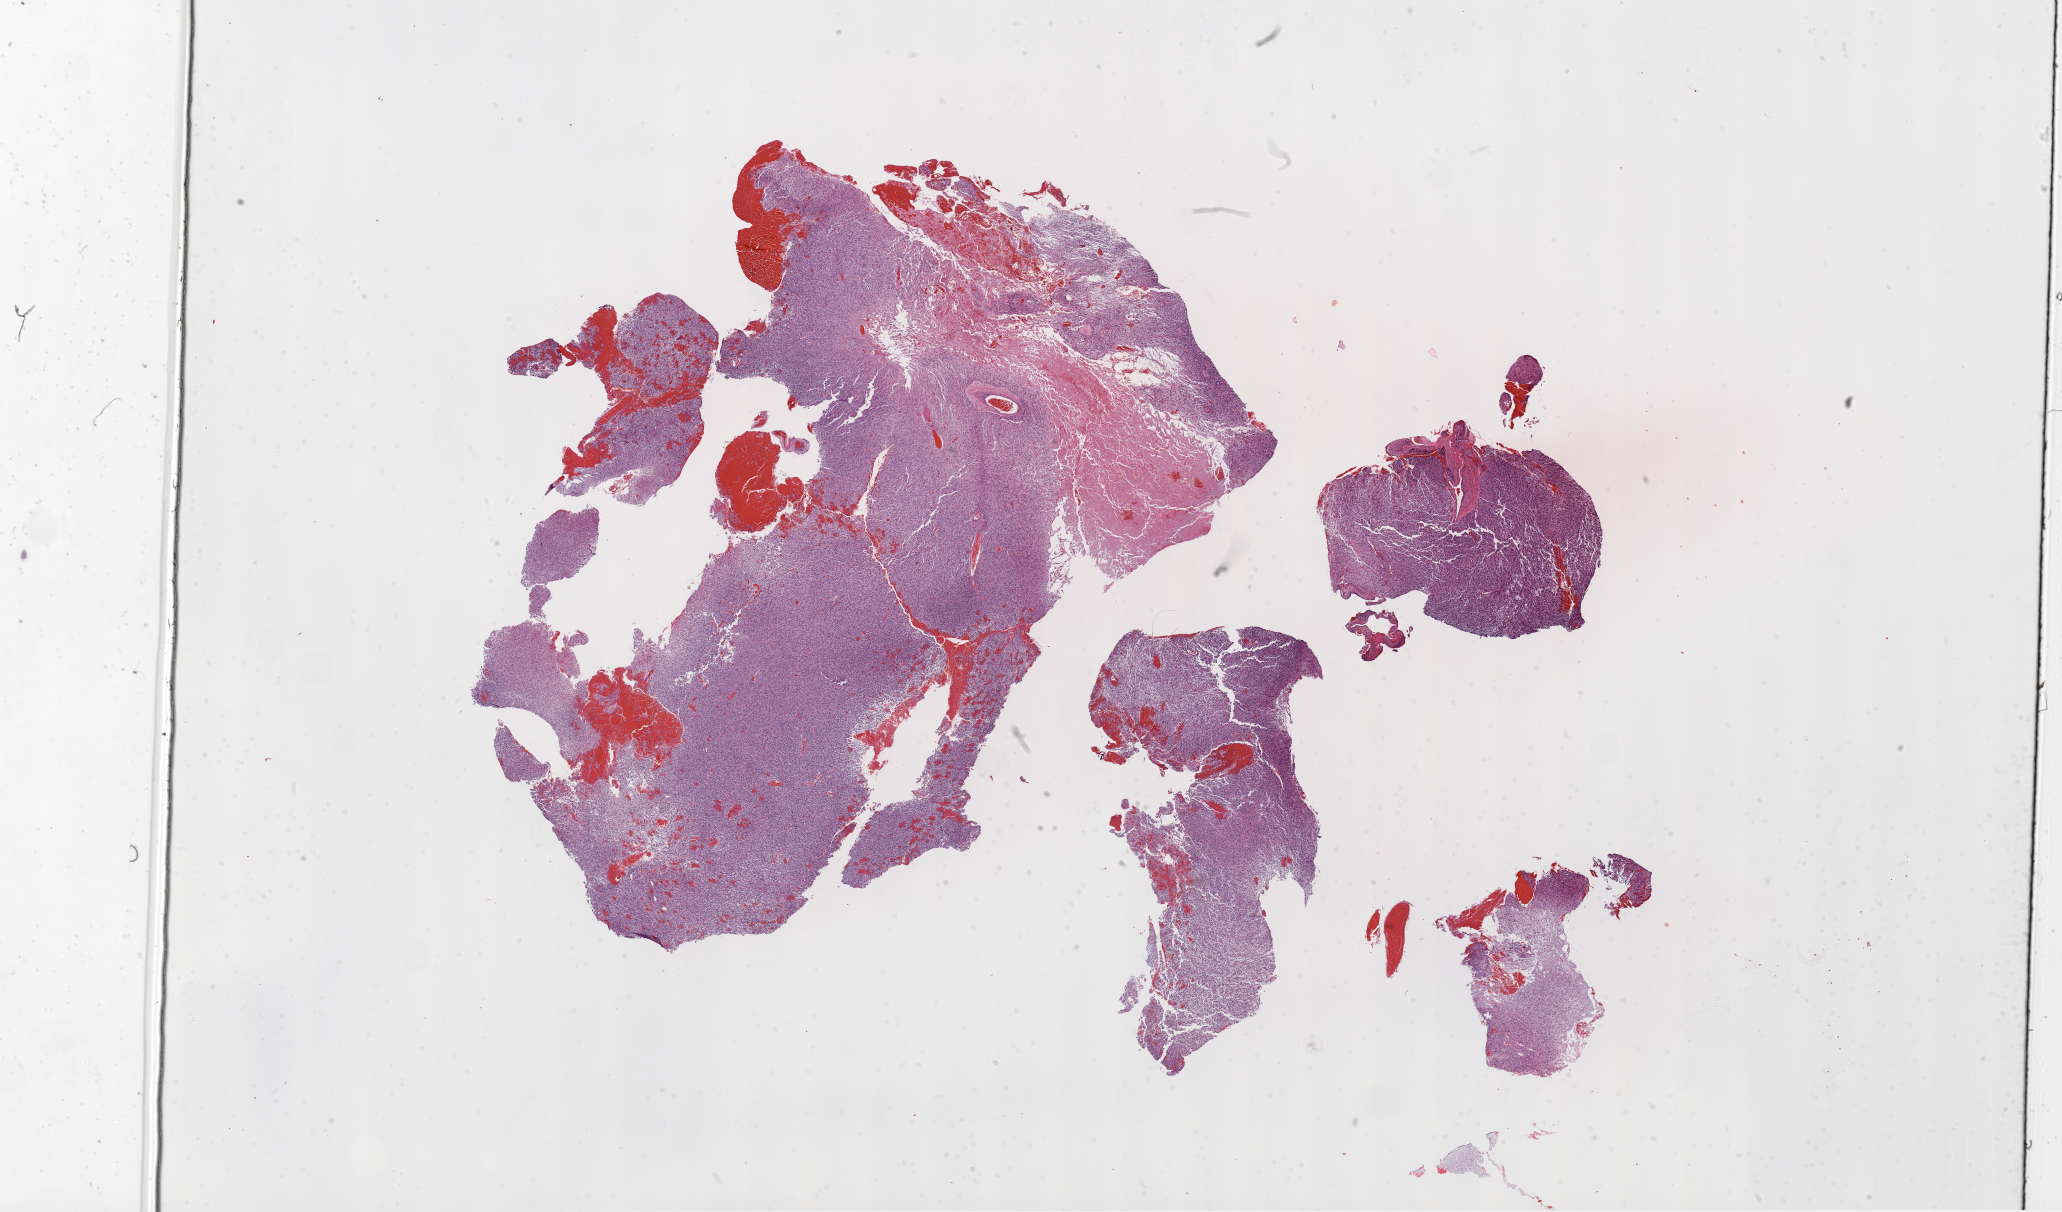
Whole-slide histology image, H&E-stained, shown as a low-resolution overview of the whole scanned area (about 33.1 x 19.5 mm, from a 20x scan); formalin-fixed paraffin-embedded (FFPE) diagnostic section; primary tumour sample from the brain. Male, age 66 years at initial diagnosis.
Histologic diagnosis: Glioblastoma.